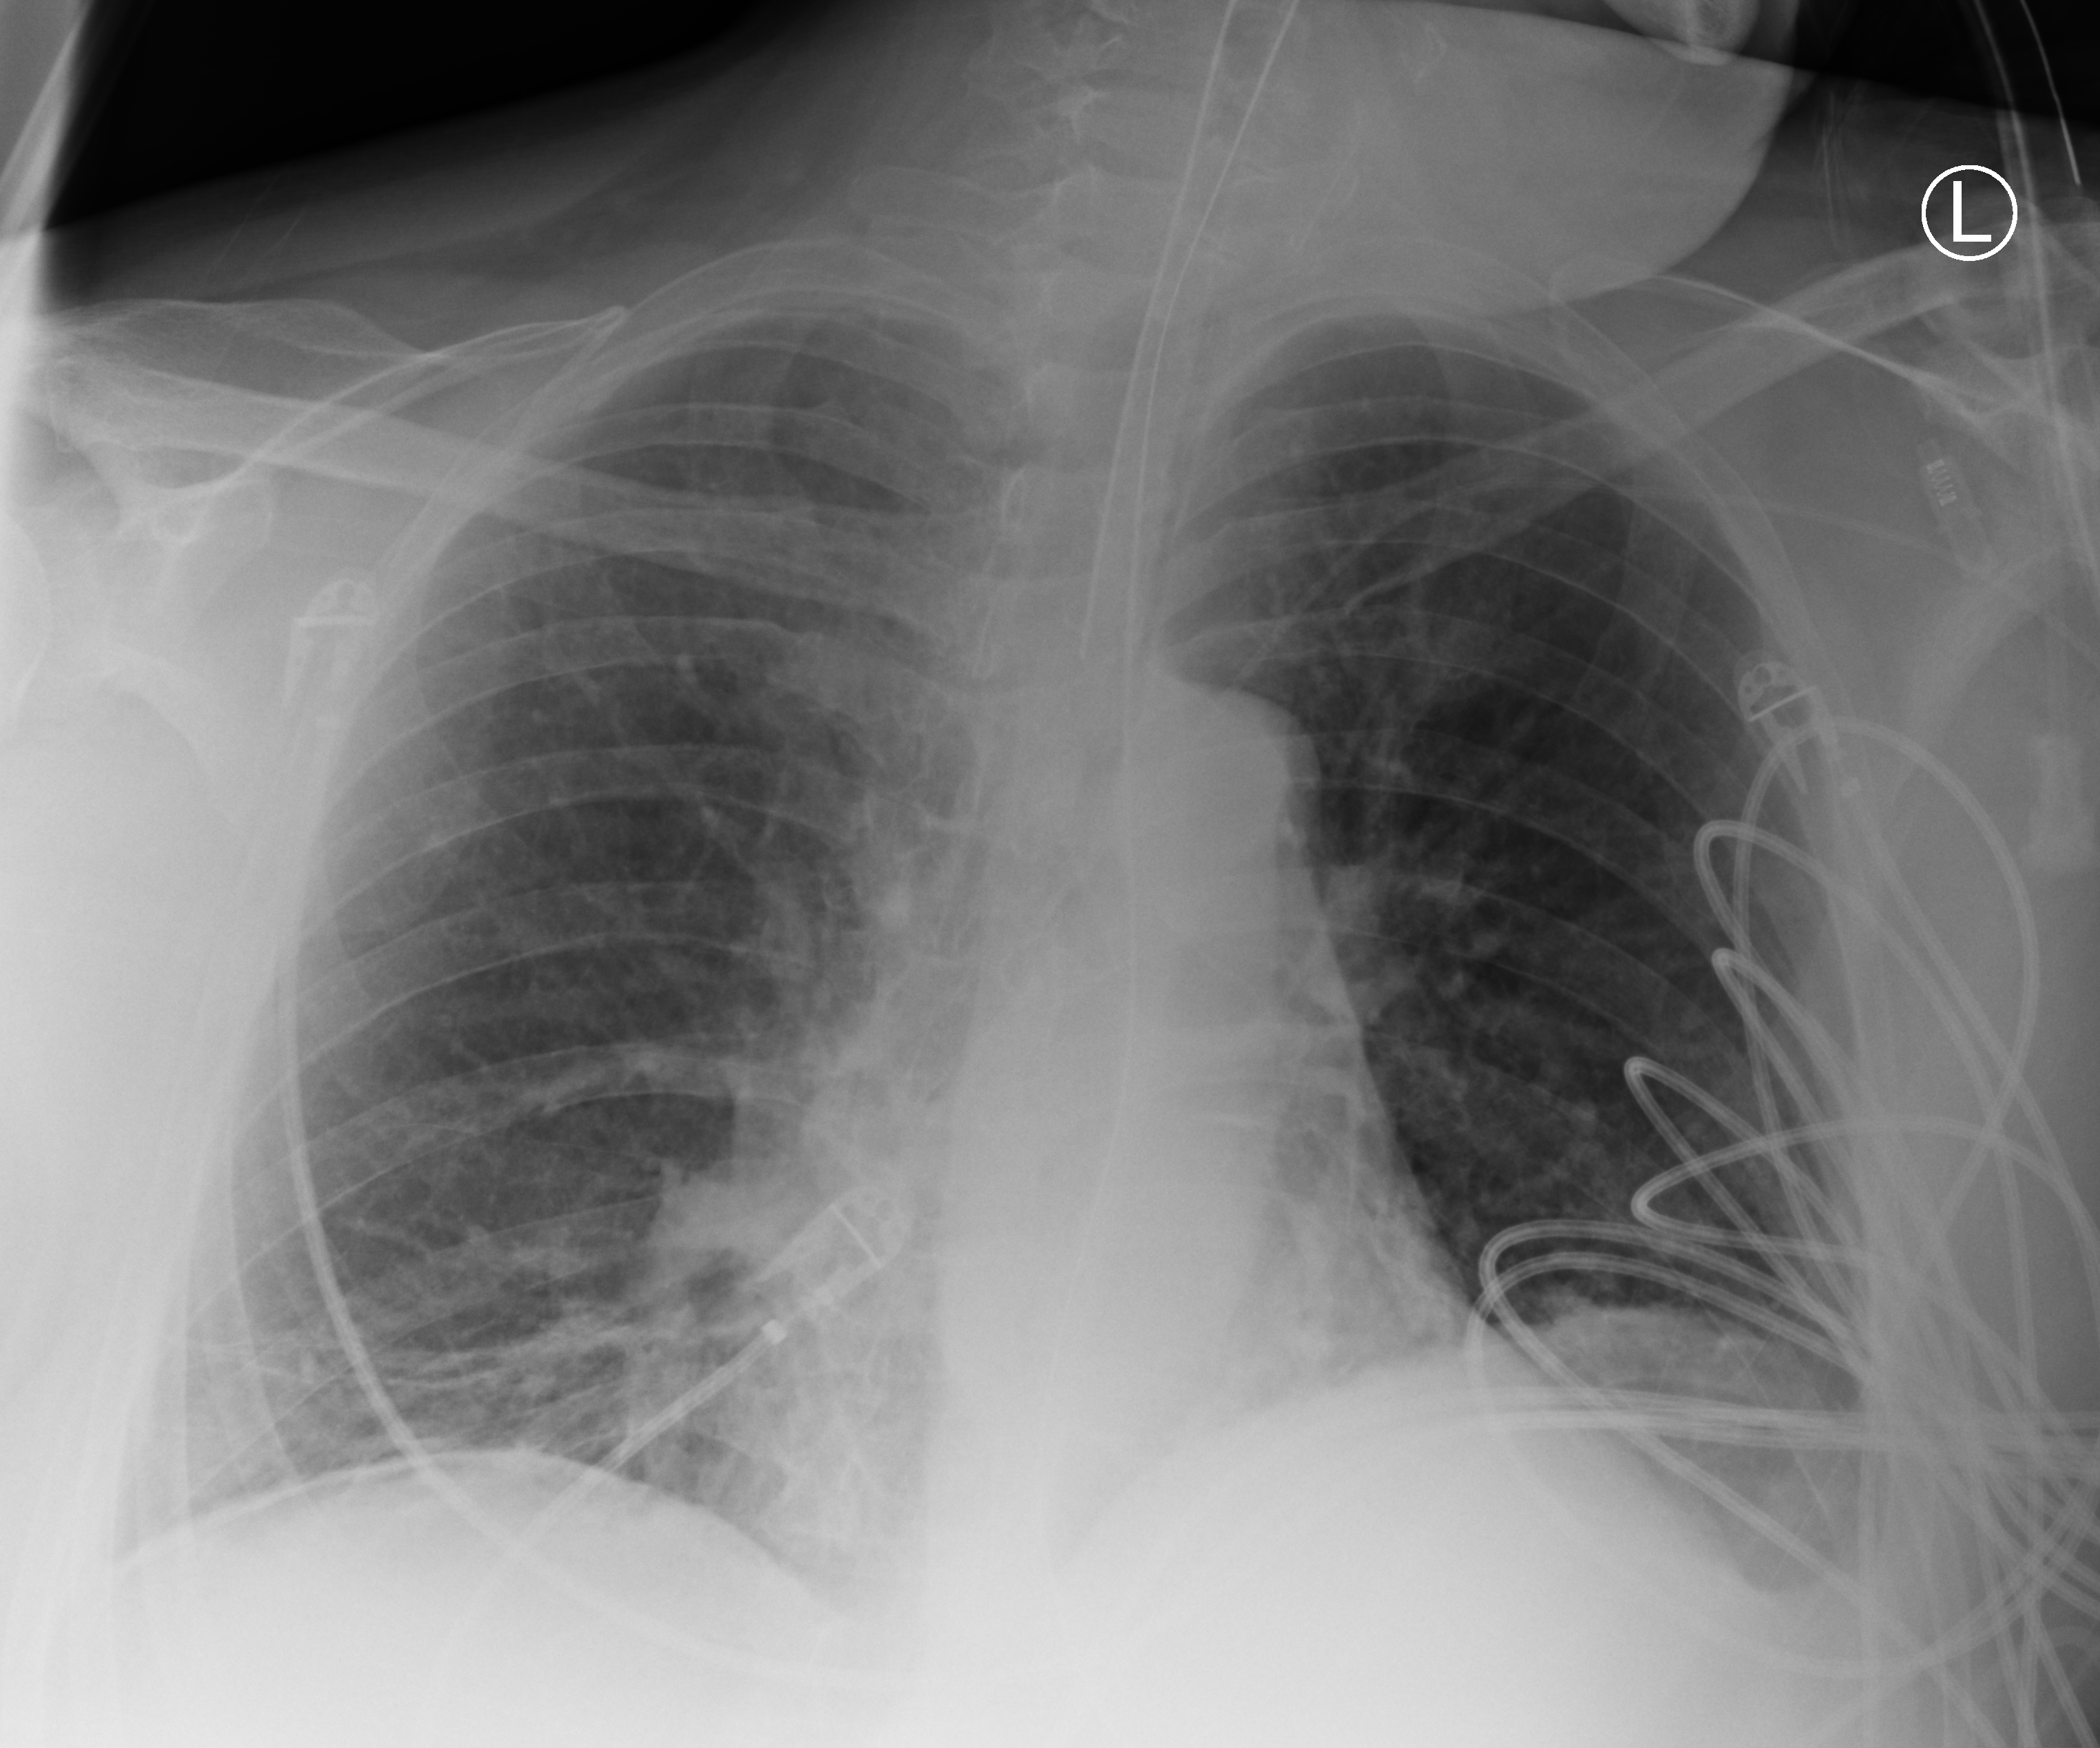
Portable chest radiograph. Patient hospitalised with COVID-19; male, aged 60–74 years.
From the hospital-stay record, not from the radiograph (when in the stay this image was taken is not recorded):
- COPD (admission record): no
- mechanically ventilated during this hospital stay: yes